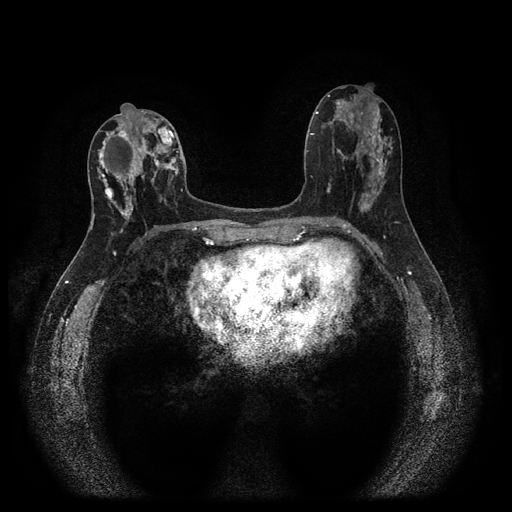
Breast MRI (dynamic contrast-enhanced, multi-phase), one axial slice; slice 48 of 116 in the series (ordered by position); dynamic contrast-enhanced series, time point 2 of 5 at this slice position (early post-contrast); 1.5 T; TE 2.7 ms, TR 5.4 ms; 2 mm slice thickness; 512 × 512 image matrix. Female patient, age 47 years.
Annotated regions visible in this slice (semi-automatic segmentation, software-assisted and operator-edited):
- breast lesion (labelled 'tumour' in the annotation; benign lesions carry a separate 'benign' label): box from (x=97, y=116) to (x=178, y=223) px
- breast lesion (labelled benign in the annotation): (x=104, y=187)–(x=115, y=200)